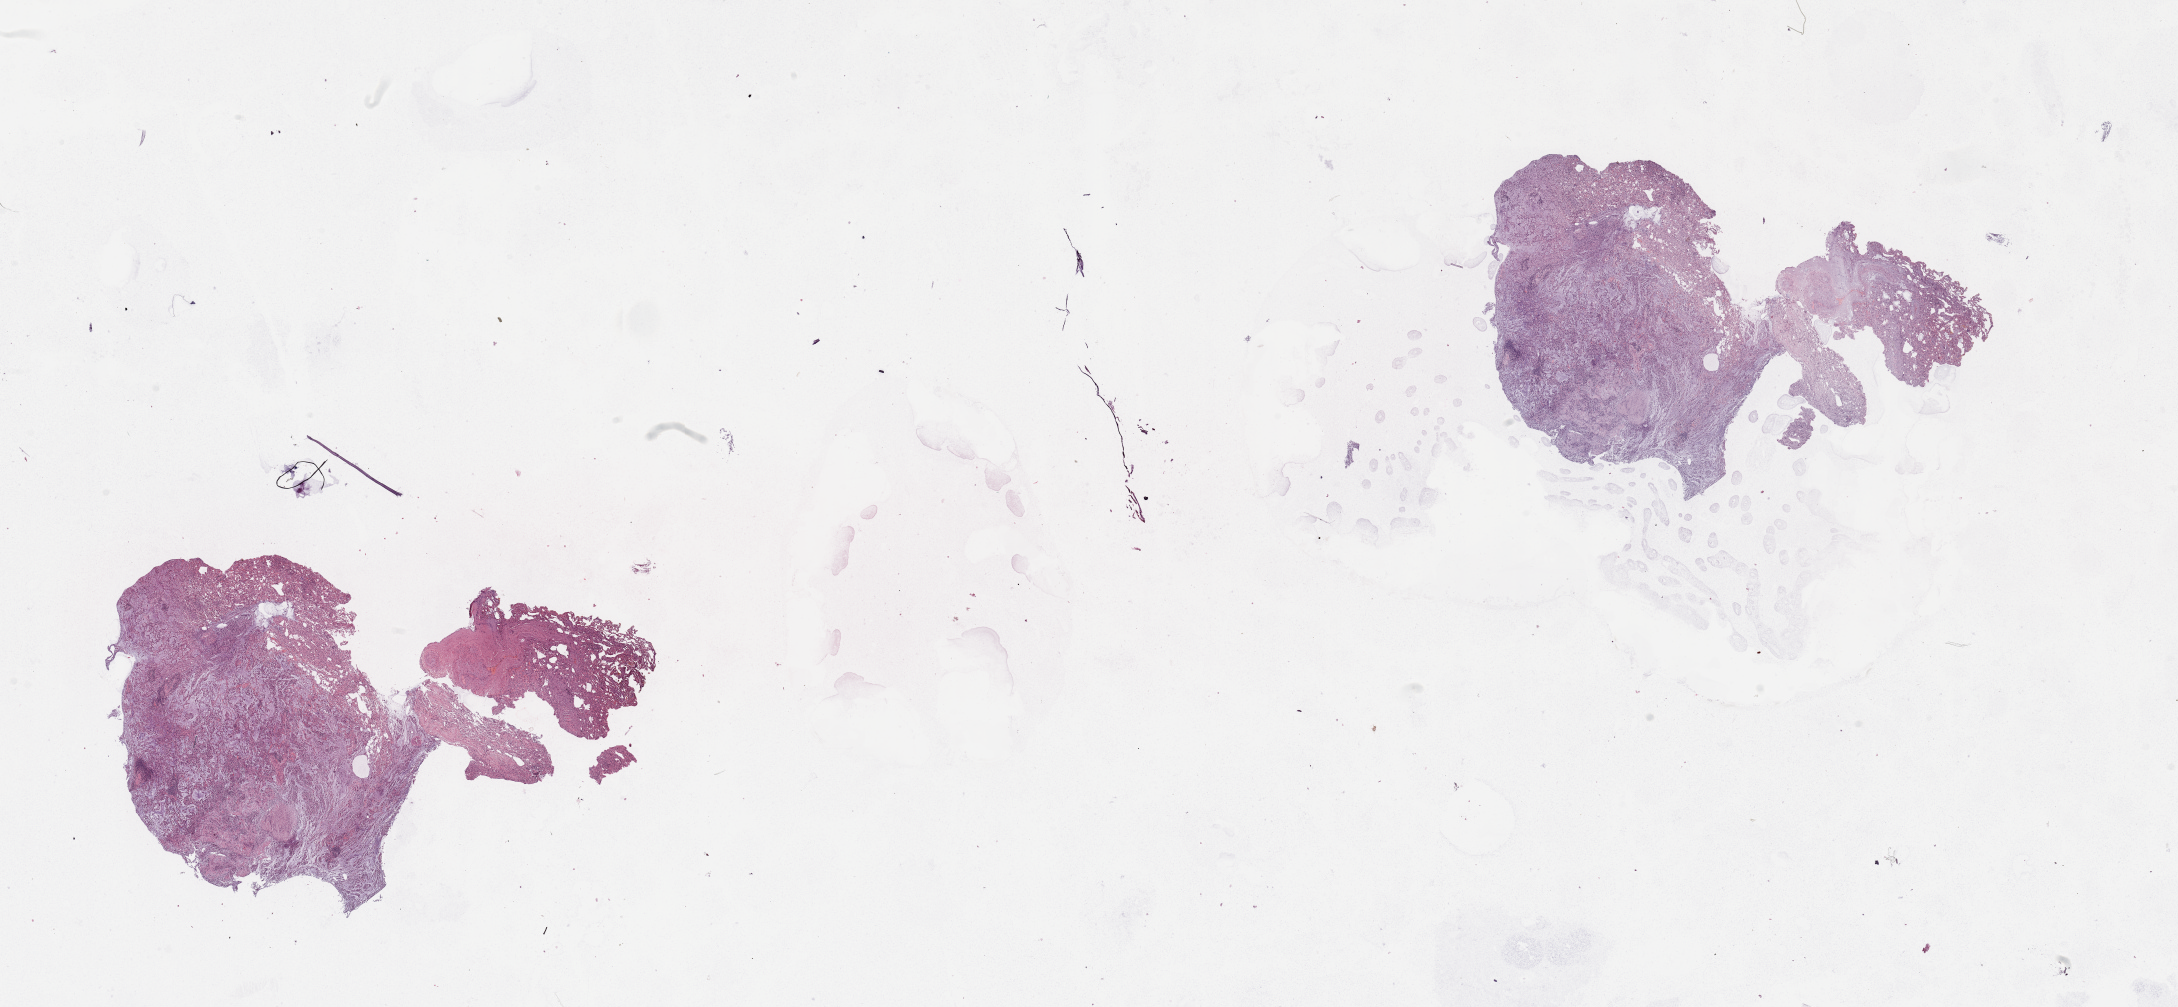
H&E-stained whole-slide image, shown as a low-resolution overview of the whole scanned area (about 34.5 x 15.9 mm, from a 20x scan). Tumour tissue sample, lung. Male, 67 y/o.
Histologic diagnosis: Adenocarcinoma, NOS.